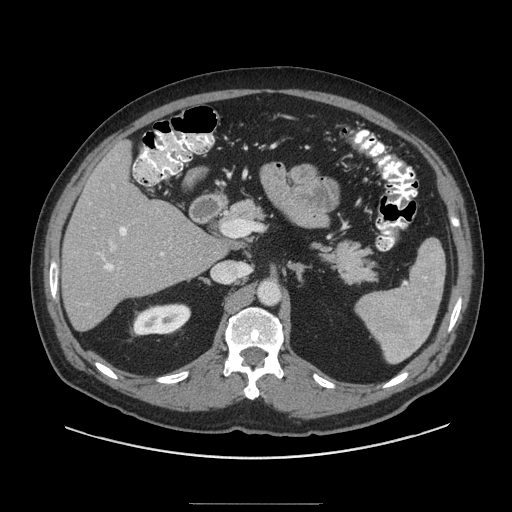
Contrast-enhanced abdominal CT (liver protocol), one axial slice; position 51 of 91 along the scan axis; 140 kVp; soft-tissue window (W 400 / L 40 HU); 2.5 mm slice thickness; 512 × 512 image matrix, field of view 440 × 440 mm. From the clinical record (not read from this slice): diagnosis: hepatocellular carcinoma (patient treated with transarterial chemoembolisation; whether this scan precedes or follows treatment is not stated here); TNM stage (as recorded): Stage-I; Child-Pugh class: A; tumour differentiation: well differentiated; tumour nodularity: uninodular.
Annotated regions visible in this slice (semi-automatic segmentation, software-assisted and operator-edited):
- liver parenchyma outside the tumour (the mass and vessels are separate outlines, so this box may not span the whole liver): bounding box (x1, y1, x2, y2) in pixels: (62, 142, 226, 330)
- liver vessels: (98, 227, 164, 271)